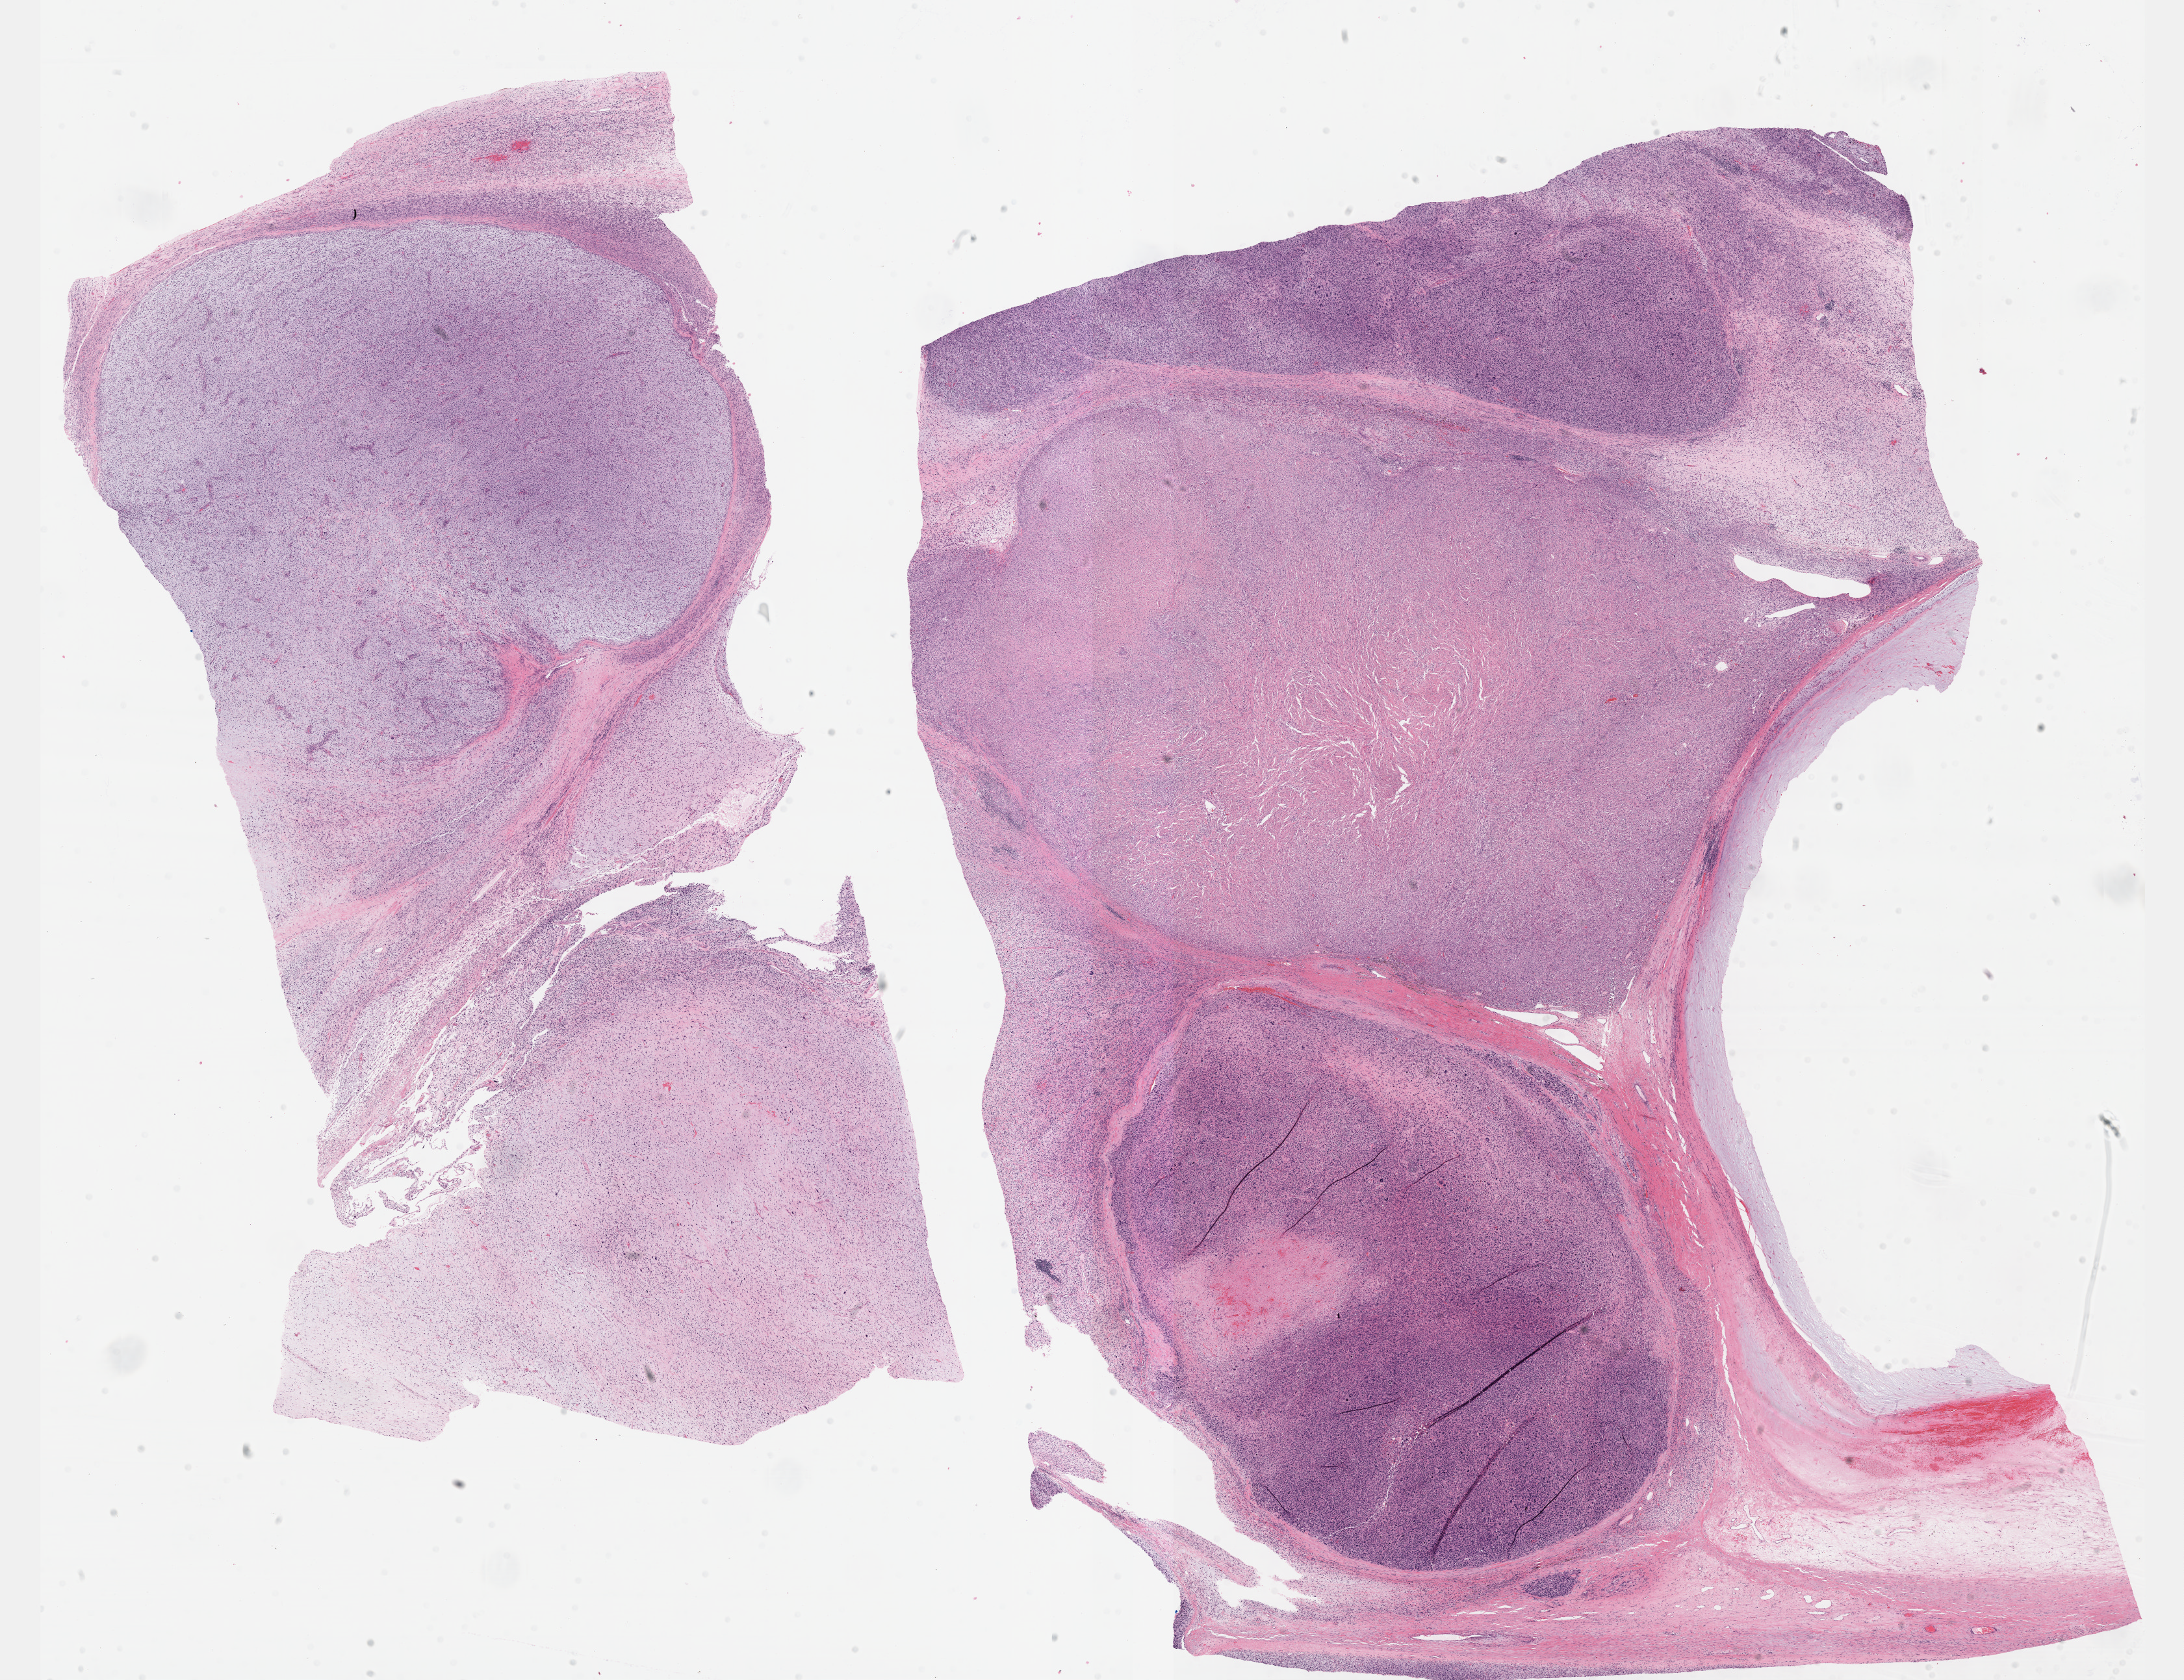
H&E-stained whole-slide image — low-resolution overview of the scanned area, about 27.2 x 20.9 mm, FFPE section, primary tumour sample from the connective, subcutaneous and other soft tissues. Patient sex: male.
Diagnosis: Fibromyxosarcoma.